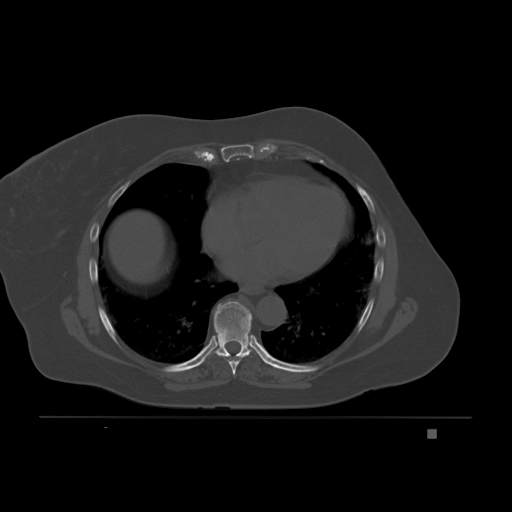
CT including the spine, one axial slice; bone window (W 1800 / L 400 HU); 3 mm slice thickness; 512 × 512 image matrix, field of view 474 × 474 mm. Female patient, age 63 years. From the clinical record (not read from this slice): primary cancer: breast.
Structures marked on this image (semi-automatically segmented with operator editing):
- T7 vertebra: bounding box [x1, y1, x2, y2] px = [218, 340, 249, 375]
- T8 vertebra: [214, 301, 253, 358]